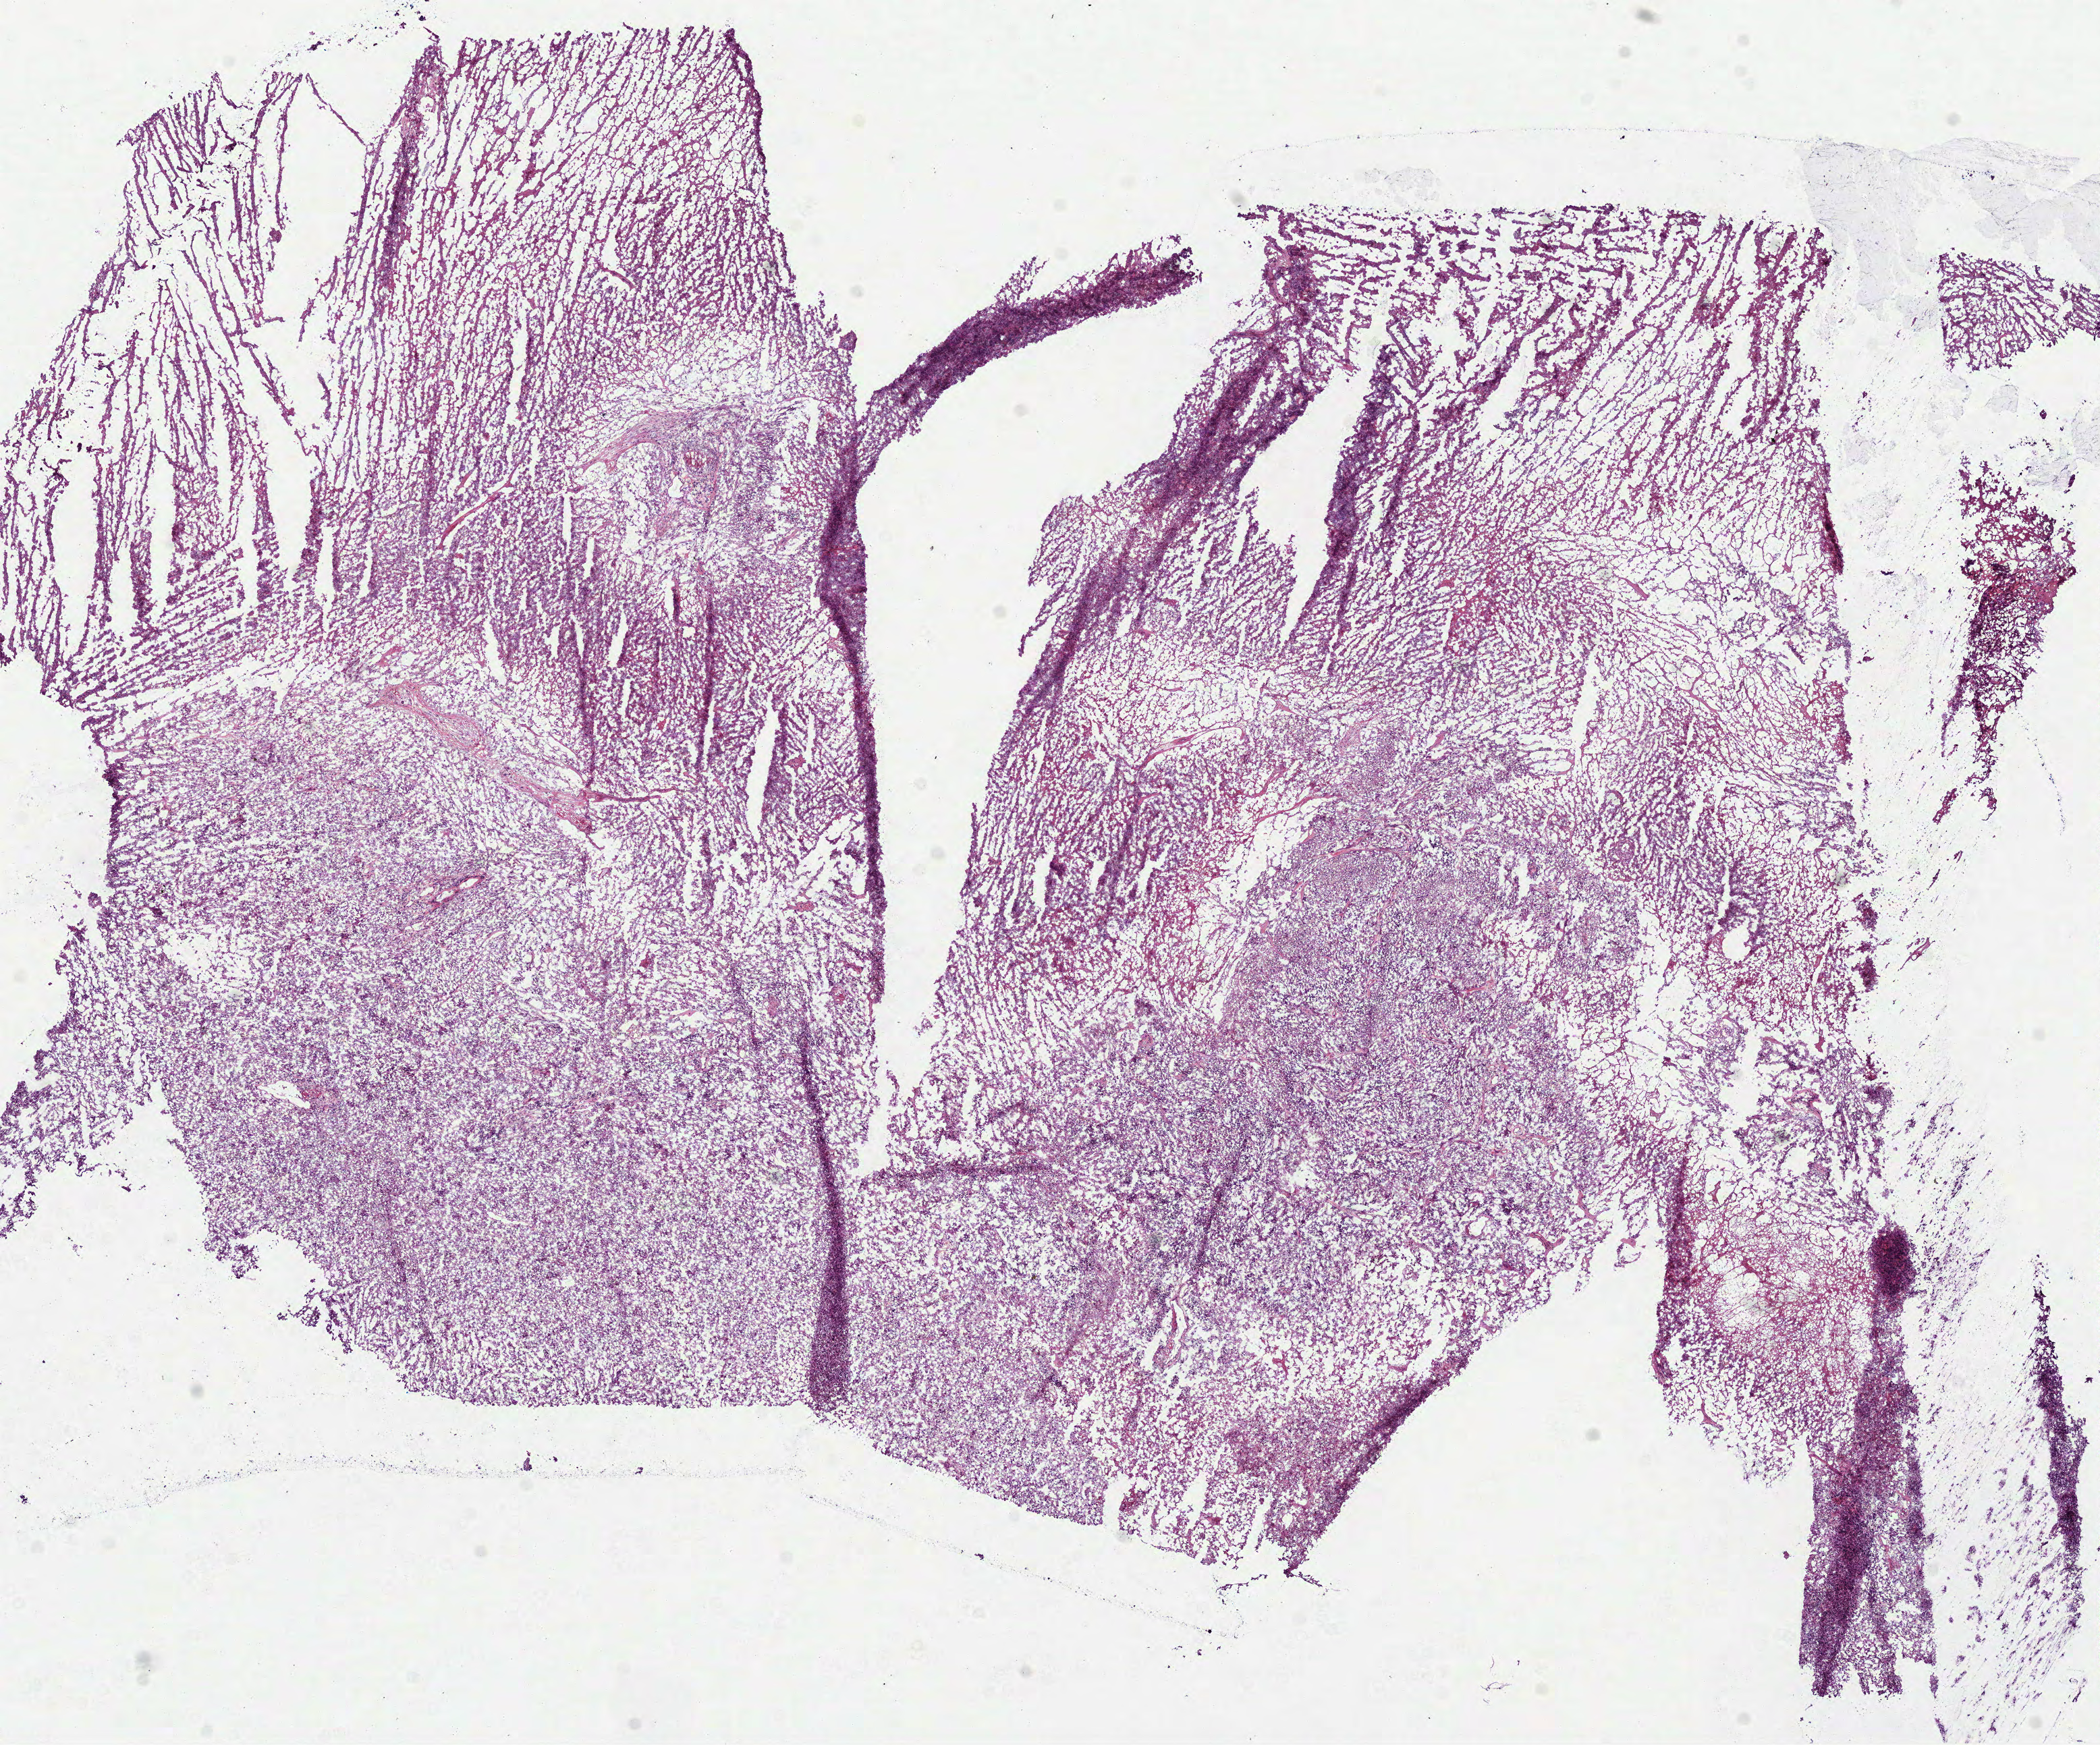
Digitized H&E tissue section (whole slide) — shown as a low-resolution overview of the whole scanned area (about 12.5 x 10.4 mm); frozen section from the bottom of the tissue portion; primary tumour sample from the brain. Male, age 58 years at initial diagnosis. Slide review estimates, as recorded: tumour cells 50%, tumour nuclei 80%, normal cells 0%, stromal cells 0%, necrosis 50%.
• histologic diagnosis: Glioblastoma